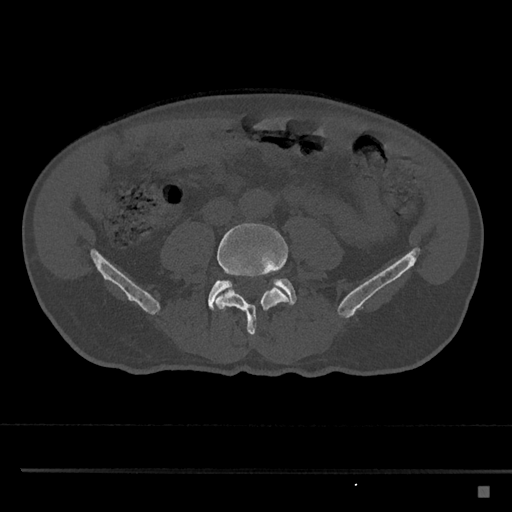
CT including the spine, one axial slice. Slice 617 of 797 in the series (ordered by position). Reconstruction kernel Br40s/3. 120 kVp. Bone window (W 1800 / L 400 HU). 0.5 mm slice thickness. 512 × 512 image matrix, field of view 391 × 391 mm. Patient: male, 59 years. From the clinical record (not read from this slice): primary cancer: prostate.
Annotated regions visible in this slice (semi-automatically segmented with operator editing):
- L4 vertebra: bounding box <216,223,289,335> (left, top, right, bottom; pixels)
- L5 vertebra: <208,278,297,311>